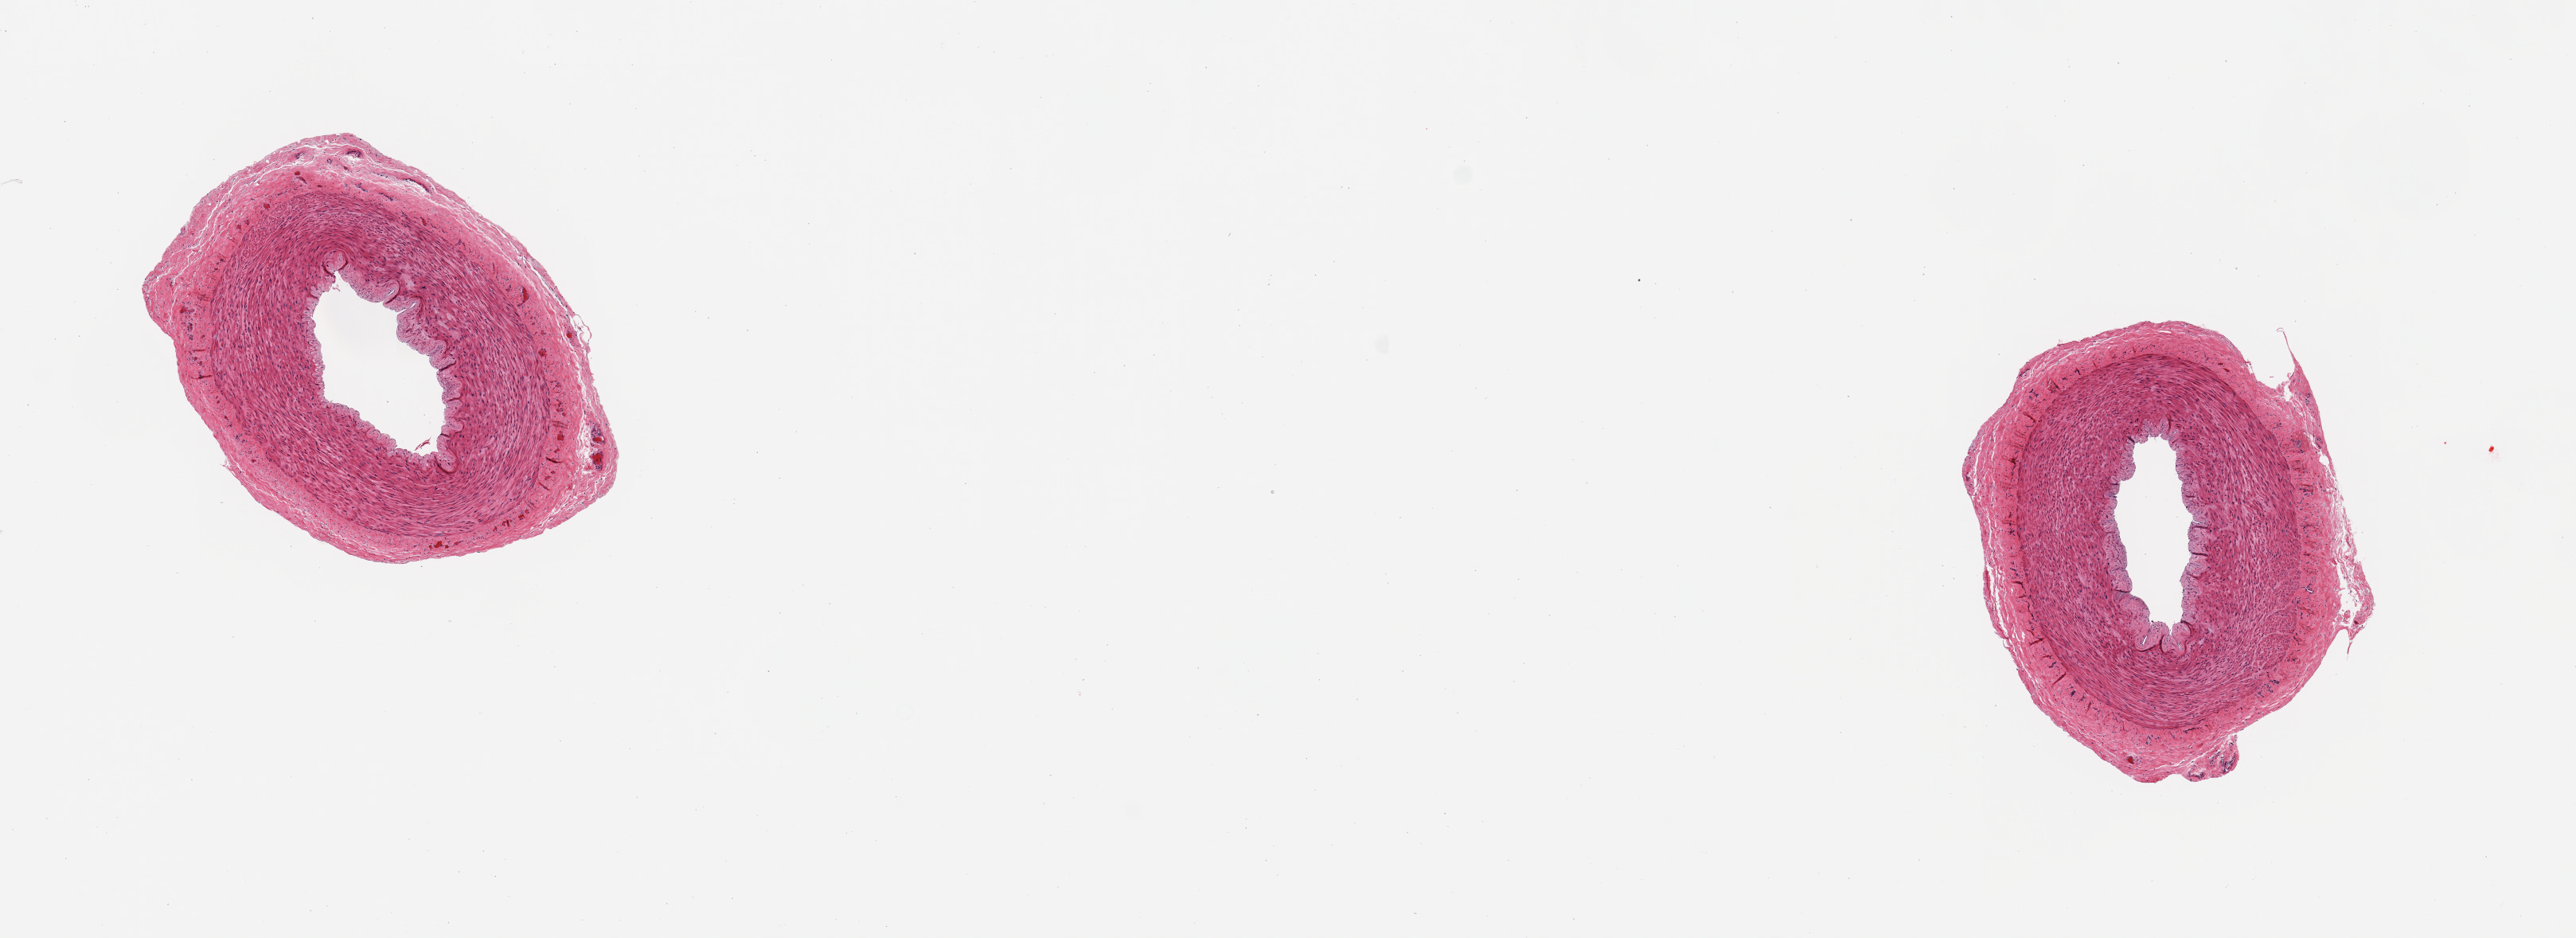
Whole-slide image, H&E stain — whole scanned area (about 12.8 x 4.7 mm) shown as a low-resolution overview, PAXgene-fixed paraffin-embedded (PFPE) section, section of tibial artery (target tissue), tissue donor sample. Donor: male.
Review note (as recorded): 2 pieces; narrow rim of adventitia (<0.3mm); no plaques.